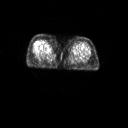
FDG PET of an extremity soft-tissue mass (from a PET/CT study), one axial slice; position 9 of 267 along the scan axis; 3.27 mm slice thickness; 128 × 128 image matrix, field of view 700 × 700 mm. Female patient, age 56 years. Case-level facts recorded for this patient, not image findings: histological type: malignant solitary fibrous tumor; grade: intermediate; site of the primary tumour: right thigh.
Structures marked on this image (expert contour drawn on MRI and transferred to this co-registered scan by the dataset authors):
- gross tumour volume including surrounding oedema: box from (x=47, y=44) to (x=48, y=45) px